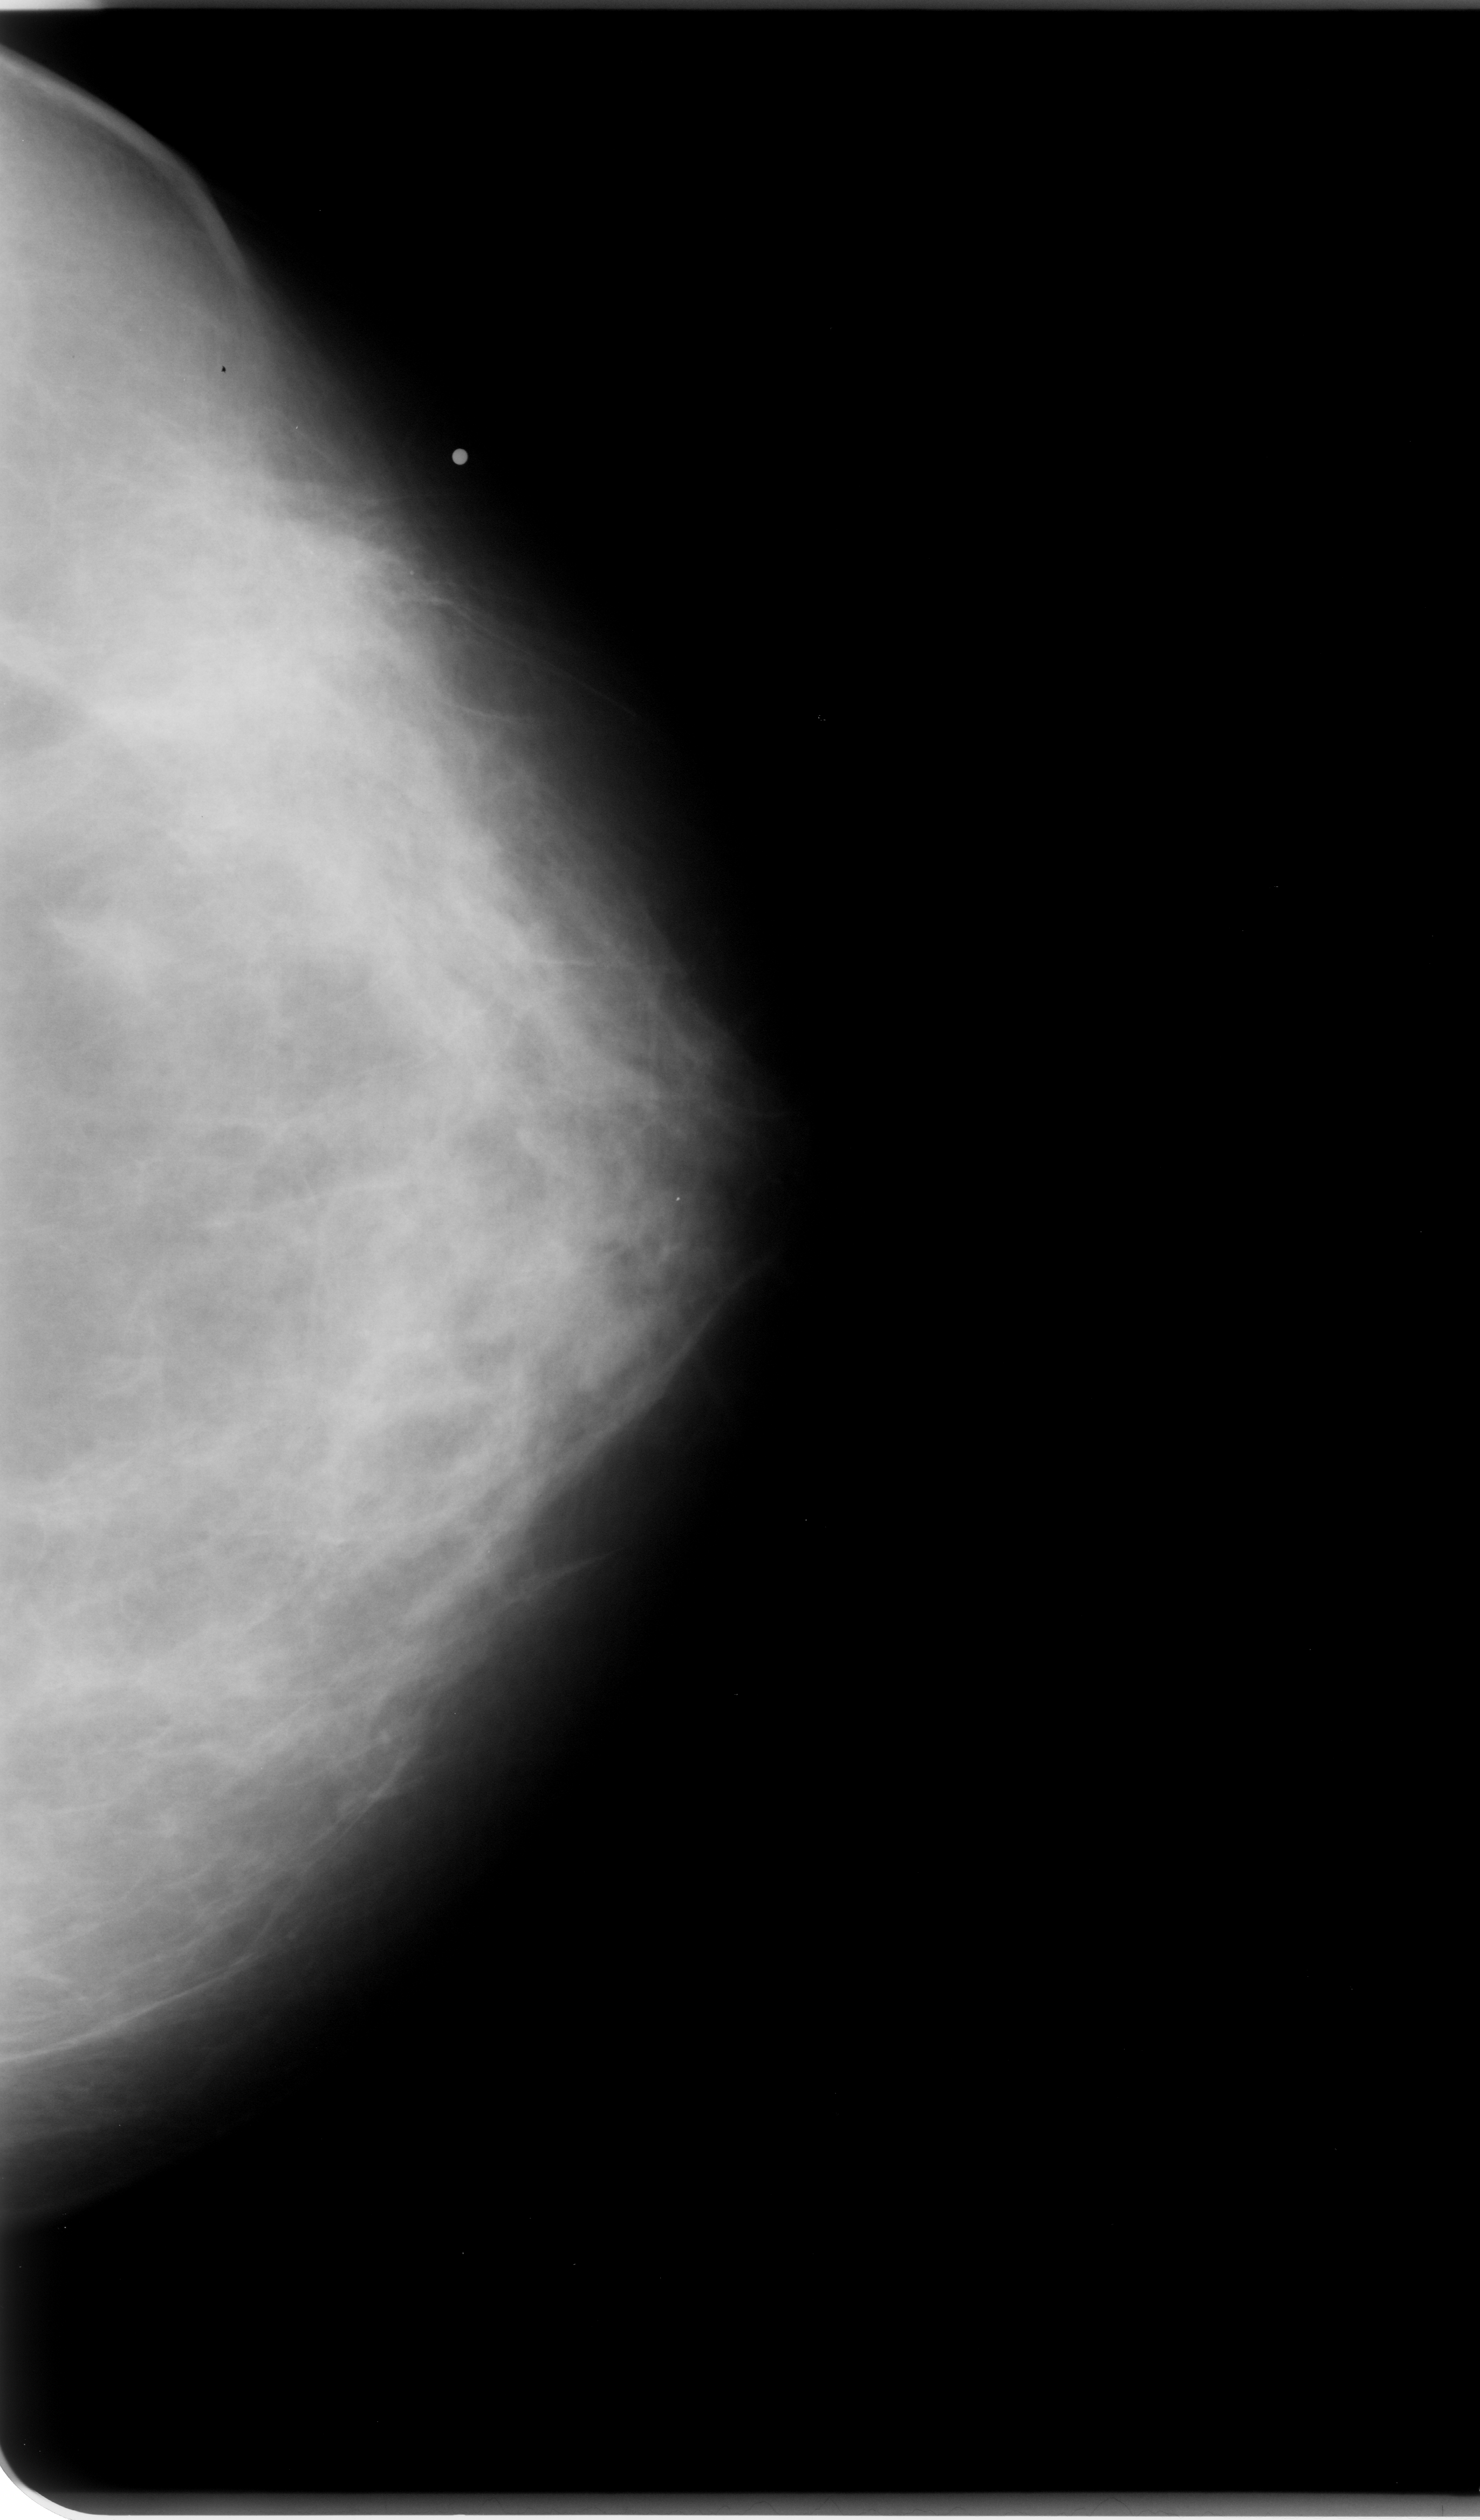
Mammogram (digitized film); left breast; craniocaudal (CC) view; BI-RADS breast density category 2 (scale 1–4); 1480 × 2520 image matrix.
Marked abnormalities (boxes around the expert regions of interest):
- calcifications, morphology amorphous, distribution clustered; BI-RADS assessment category 4; subtlety rating 2 on a 1 (subtle) to 5 (obvious) scale; pathology (as recorded): malignant: bounding box (x1, y1, x2, y2) in pixels: (81, 375, 502, 782)